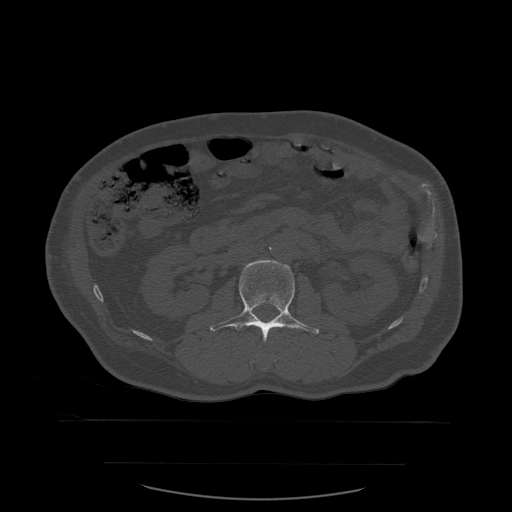
CT including the spine, one axial slice; position 220 of 590 along the scan axis; bone window (W 1800 / L 400 HU); 512 × 512 image matrix, field of view 479 × 479 mm. Patient age 71 years. From the clinical record (not read from this slice): primary cancer: lung.
Structures marked on this image (semi-automatically segmented with operator editing):
- L2 vertebra: bounding box [x1, y1, x2, y2] px = [210, 260, 320, 342]